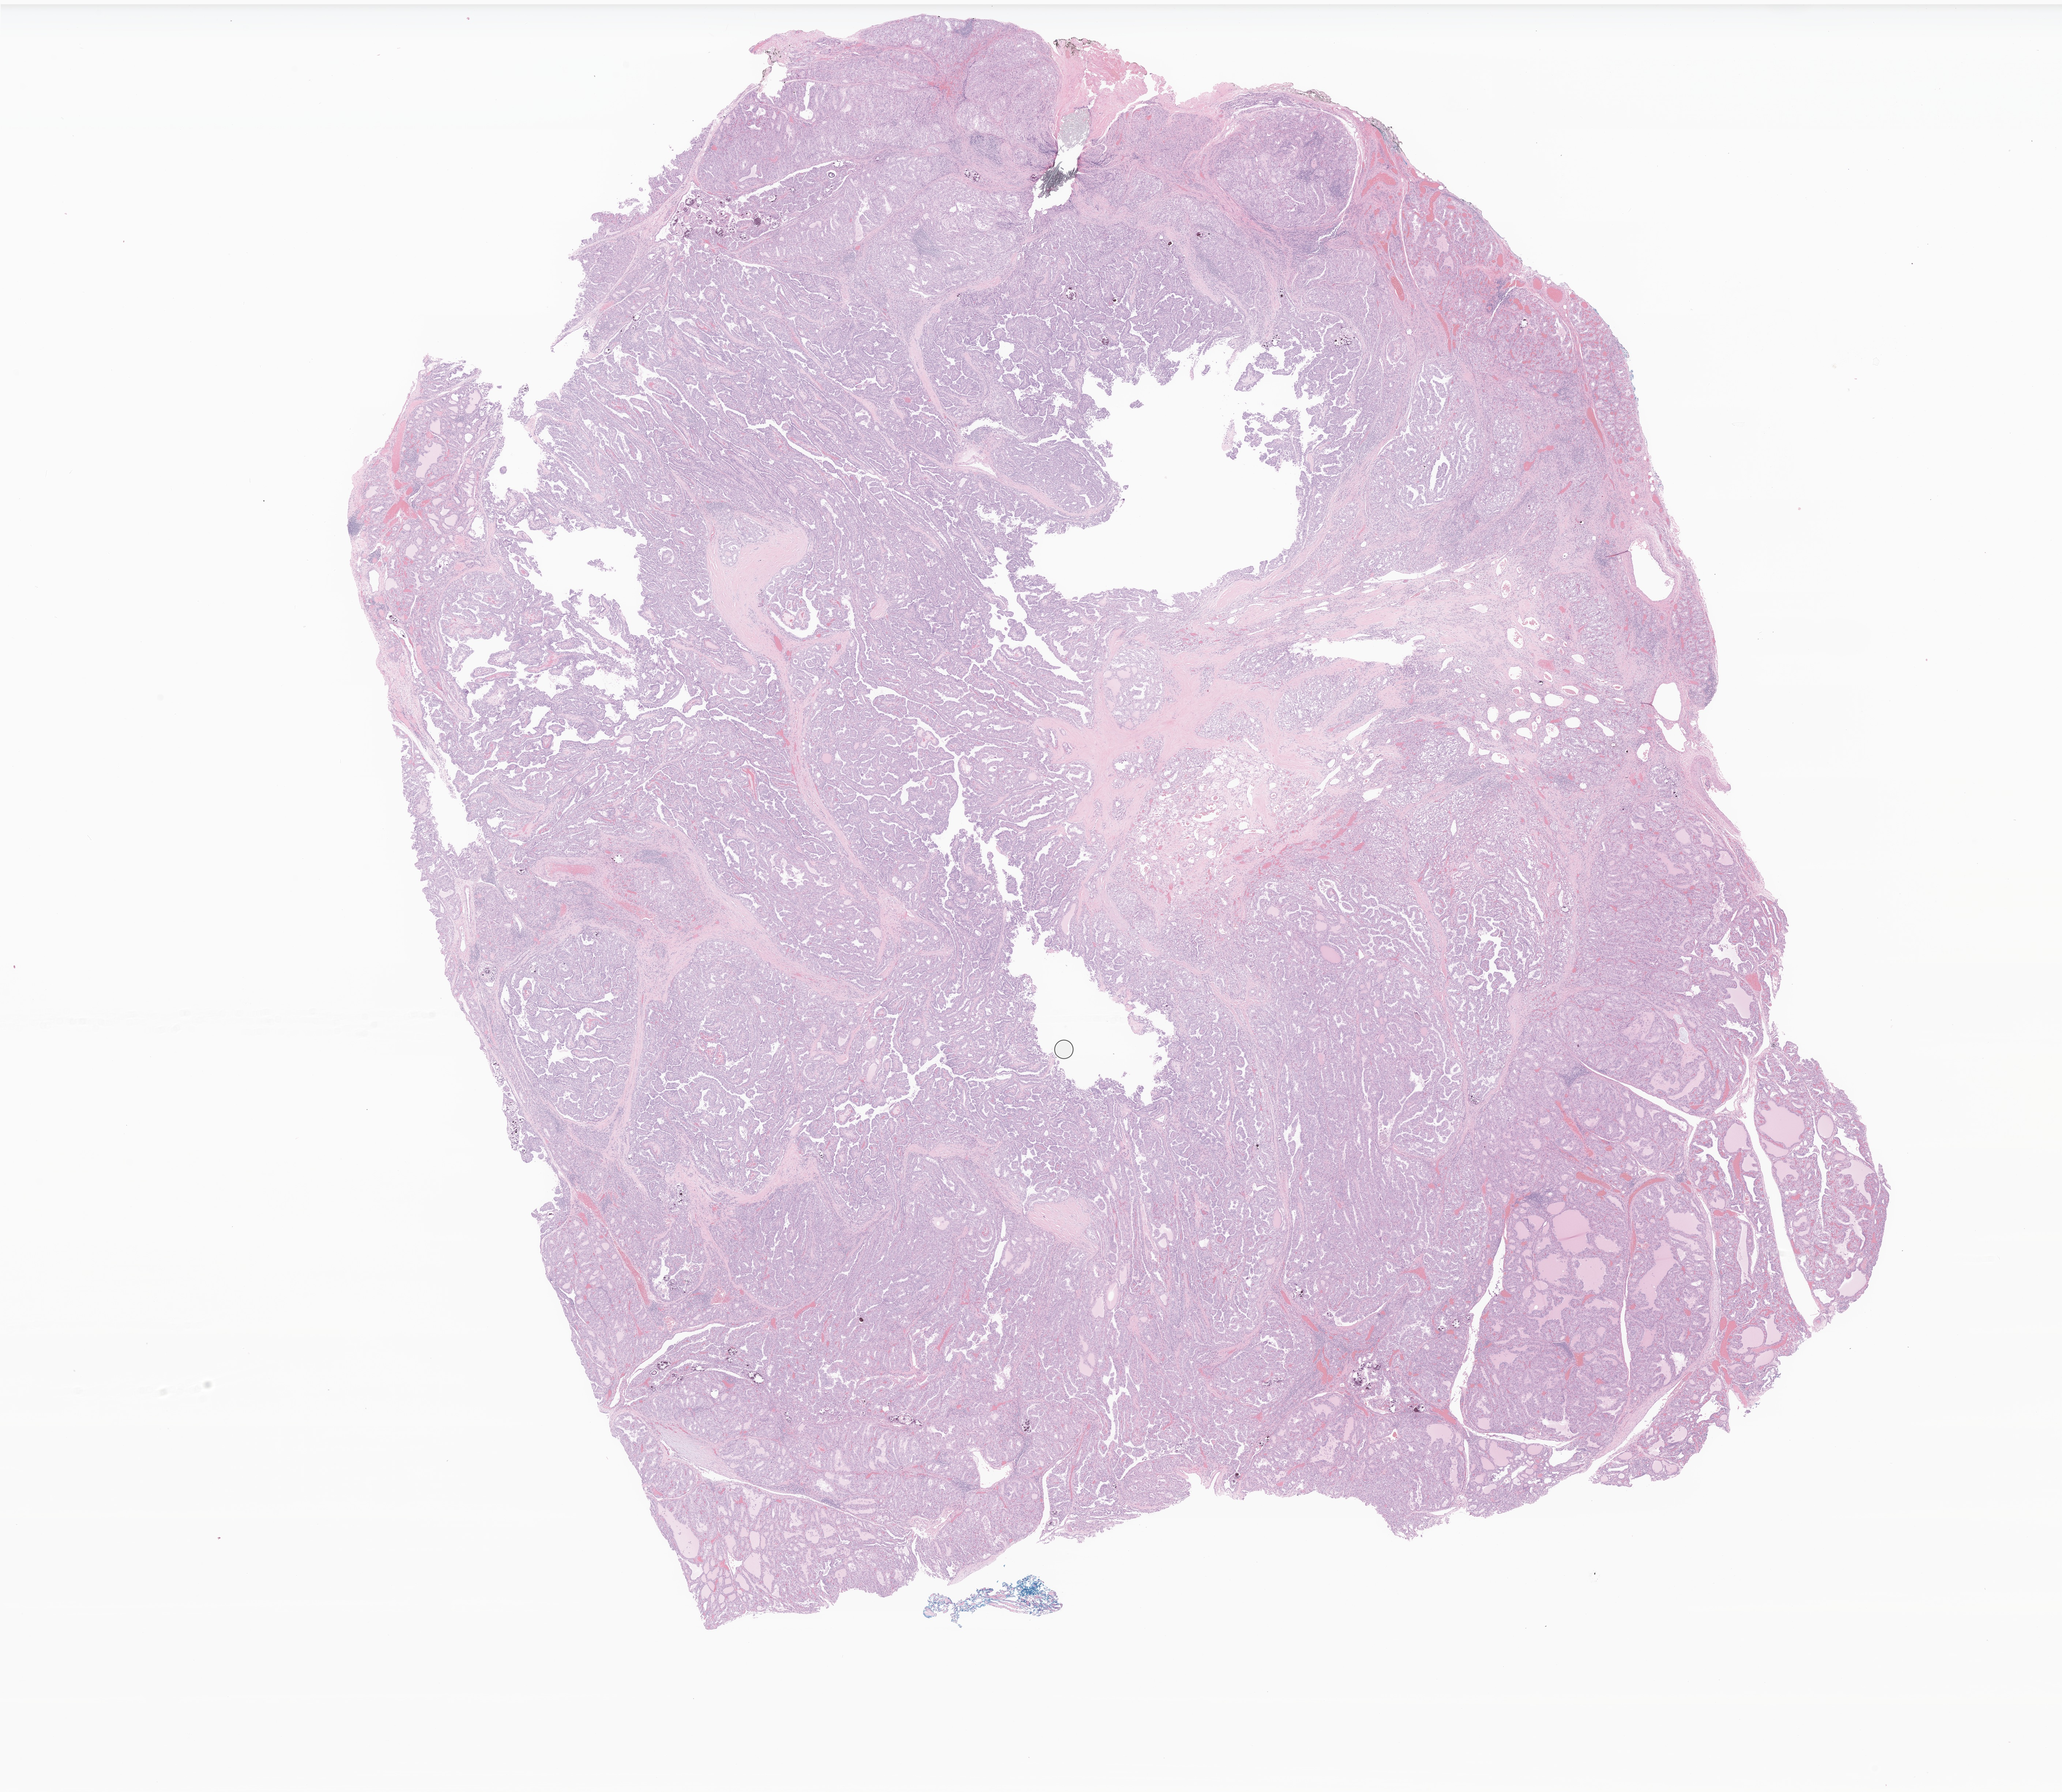
Whole-slide image, H&E stain of tumor tissue from the thyroid, shown as a low-resolution overview of the whole scanned area (about 23.8 x 20.7 mm). FFPE section. Patient: female, age 214 months (17 years 10 months).
Diagnosis (ICD-O-3 morphology term): Papillary carcinoma, NOS.